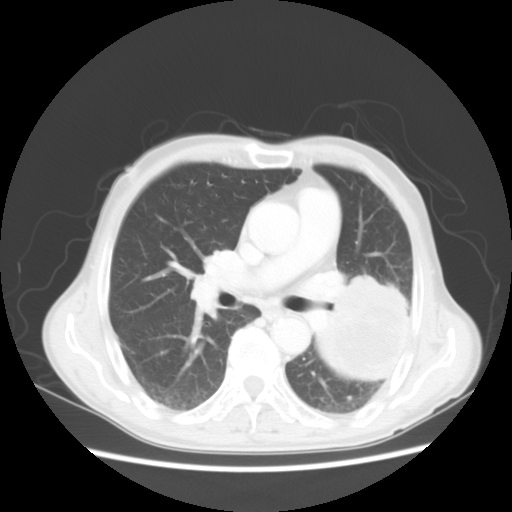
Chest CT, one axial slice; slice 28 of 51 in the series (ordered by position); lung window (W 1500 / L -600 HU); 5 mm slice thickness; 512 × 512 image matrix, field of view 360 × 360 mm. Male patient, age 64 years. Case-level facts recorded for this patient, not image findings: clinical TNM (as recorded): T4 N0 M0; histopathological grade: G2-3.
Structures marked on this image (rectangle marked by the reading radiologist):
- lung tumour (recorded histology: squamous cell carcinoma): box from (x=304, y=256) to (x=422, y=399) px